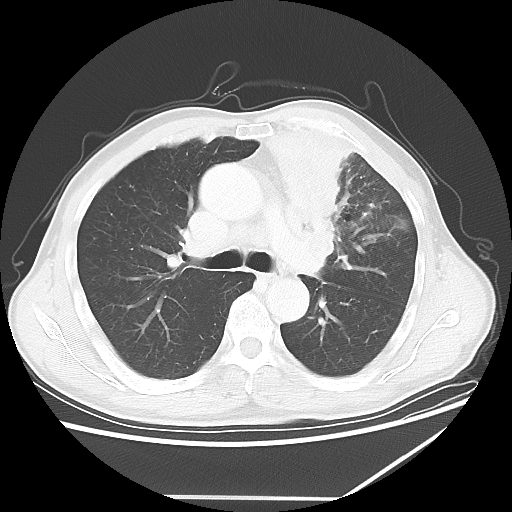
Chest CT, one axial slice; position 40 of 64 along the scan axis; reconstruction kernel LUNG; 100 kVp; lung window (W 1500 / L -600 HU); 512 × 512 image matrix, field of view 383 × 383 mm. Male patient, age 64 years. From the clinical record (not read from this slice): clinical TNM (as recorded): T1c N1 M1; histopathological grade: G2.
Annotated regions visible in this slice (rectangle marked by the reading radiologist):
- lung tumour (recorded histology: squamous cell carcinoma): box from (x=266, y=126) to (x=381, y=272) px